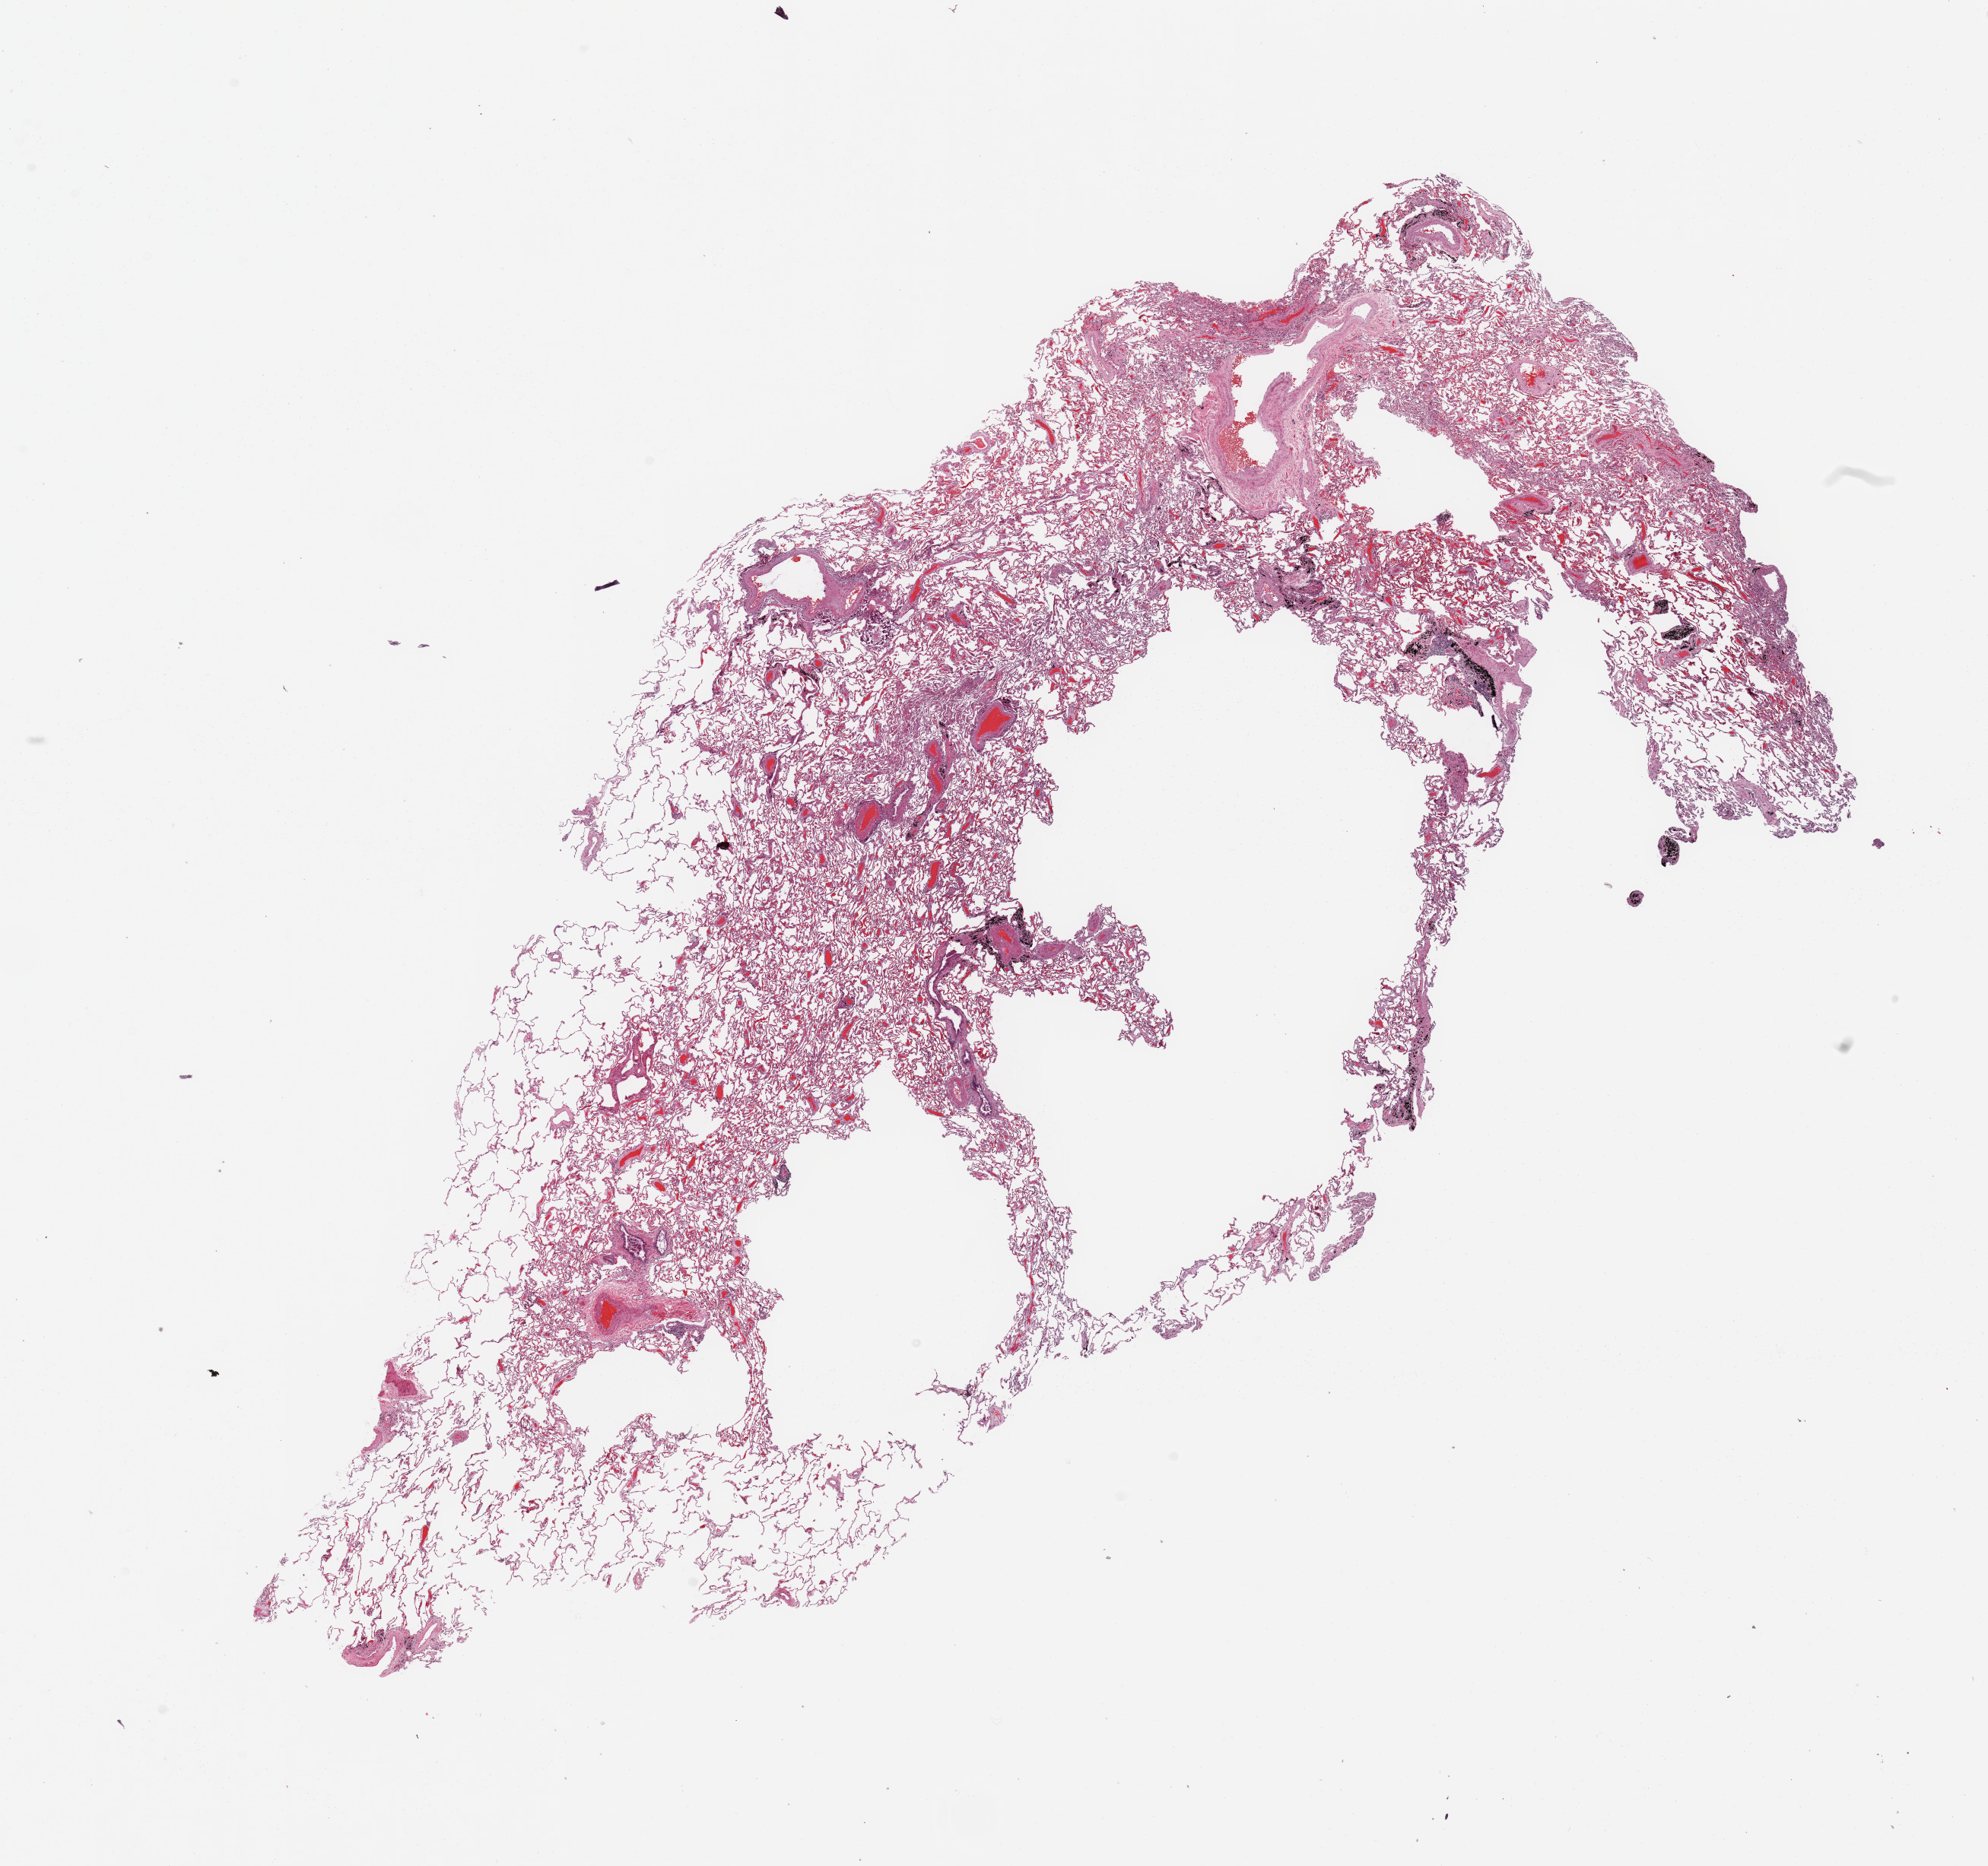
Hematoxylin and eosin (H&E) stained whole-slide image, a low-resolution overview of the entire scanned area, about 20.7 x 19.4 mm (from a 20x scan), normal (non-tumour) tissue sample, sampled site: lung. Male, 66 y/o.
* this section: normal (non-tumour) tissue from the same patient
* patient diagnosis: Squamous cell carcinoma, NOS